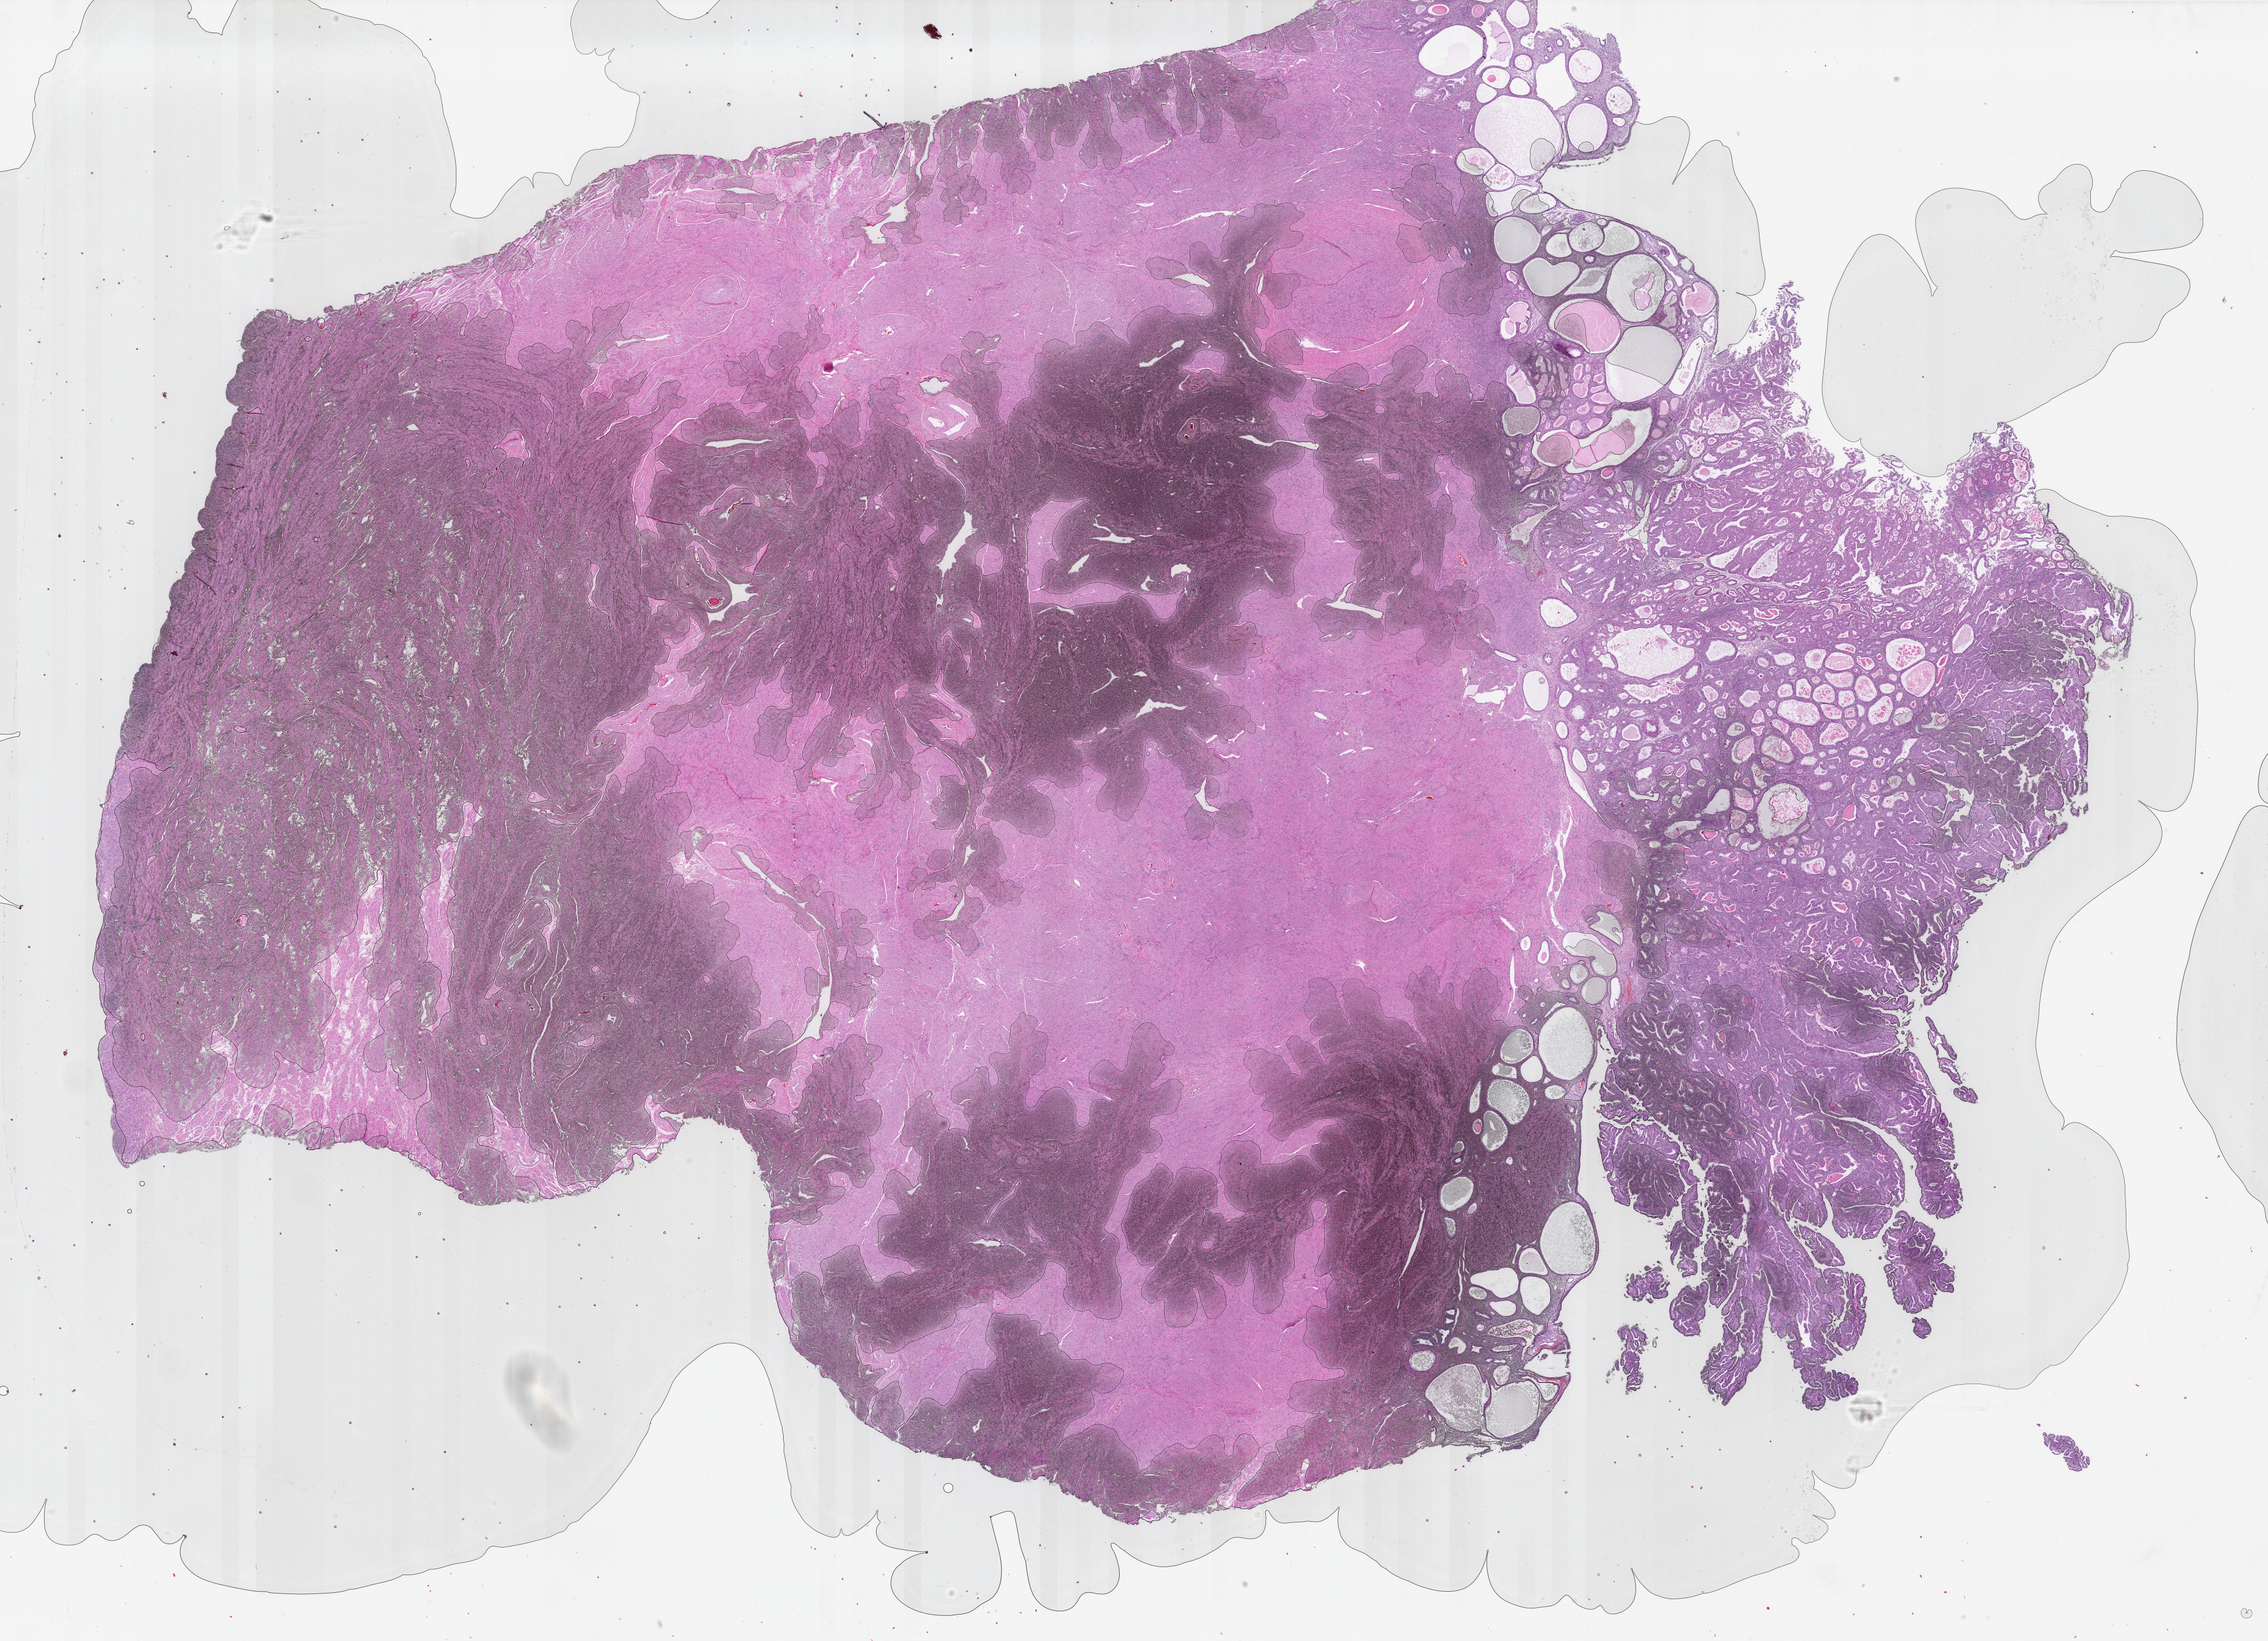
Whole-slide histology image, Hematoxylin and eosin (H&E) stained, a low-resolution overview of the entire scanned area, about 31.4 x 22.7 mm. FFPE section. Sample: primary tumour, uterus. Female, age 71 years at initial diagnosis. Histologic grade: G1 (well differentiated).
Histologic diagnosis: Endometrioid adenocarcinoma, NOS (endometrium). FIGO stage: IA.